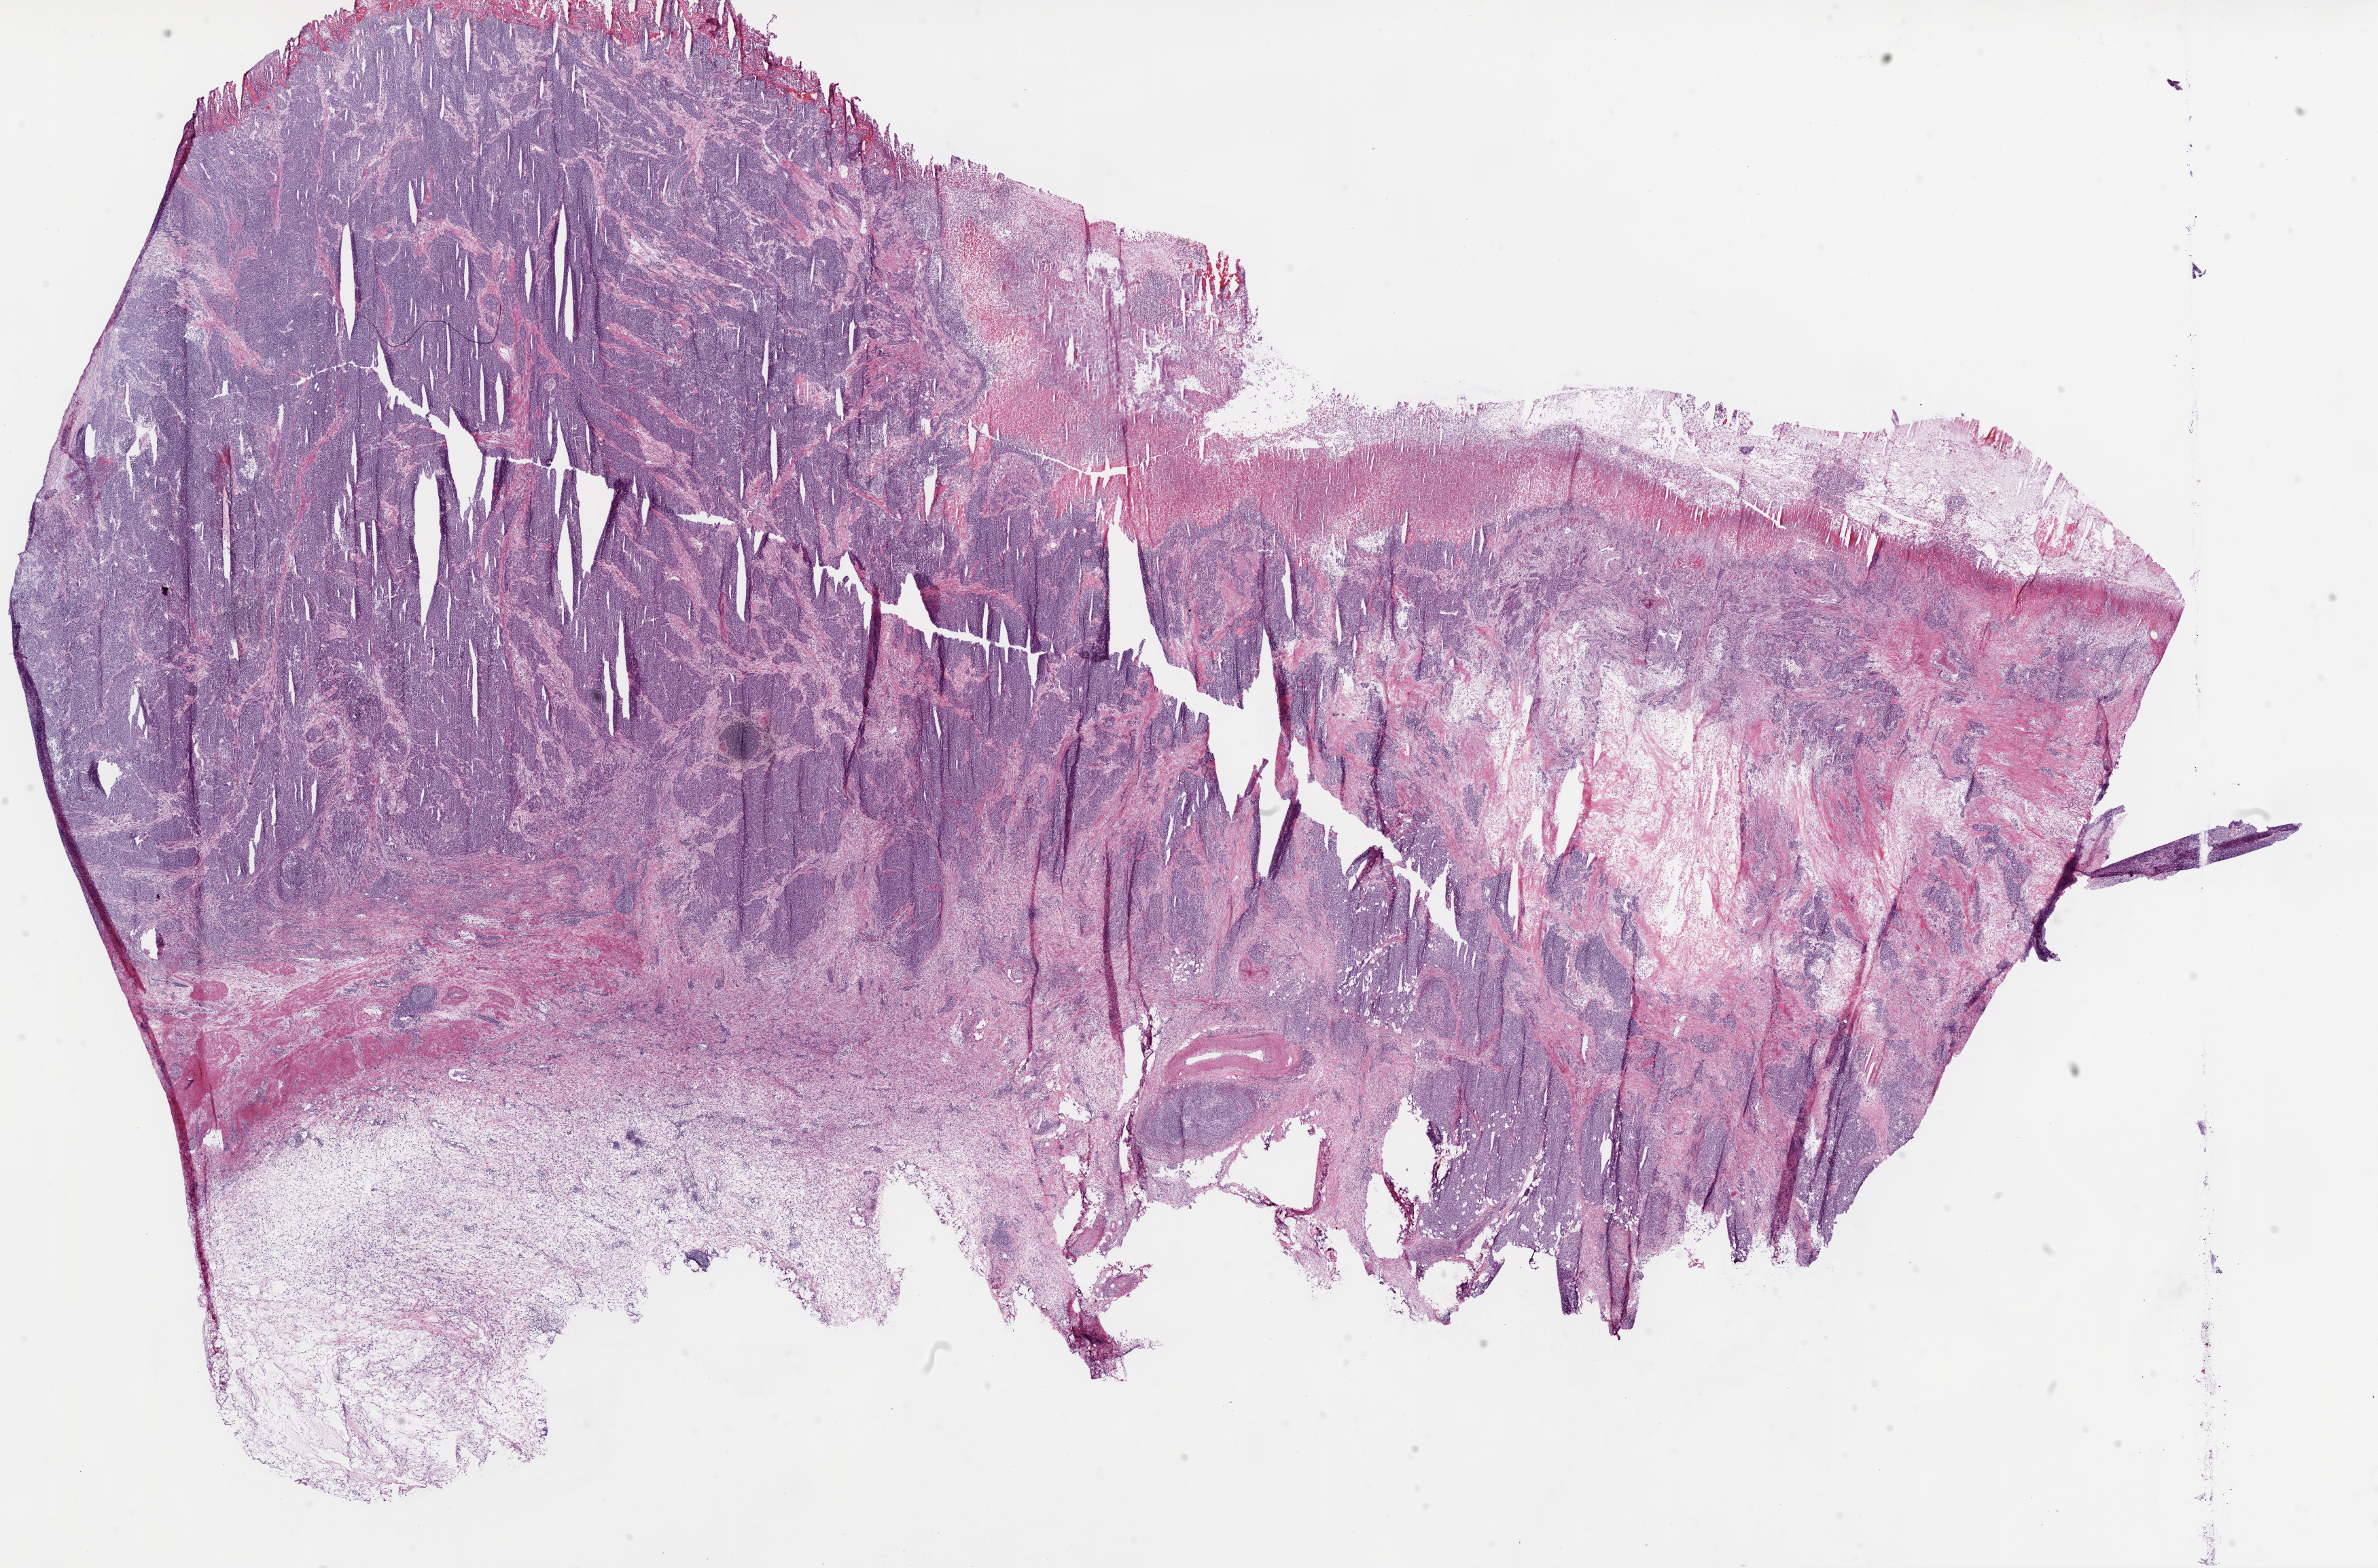
H&E-stained whole-slide image, a low-resolution overview of the entire scanned area, about 28.1 x 18.5 mm (from a 20x scan). Frozen section from the bottom of the tissue portion. Sample: primary tumour, stomach. Patient: female, age at initial diagnosis 60 years. Histologic grade: G3 (poorly differentiated). Pathologist review of this section (percent, as recorded): tumour cells 70%, tumour nuclei 80%, normal cells 0%, stromal cells 20%, necrosis 10%.
Diagnosis: Adenocarcinoma, NOS (body of stomach).